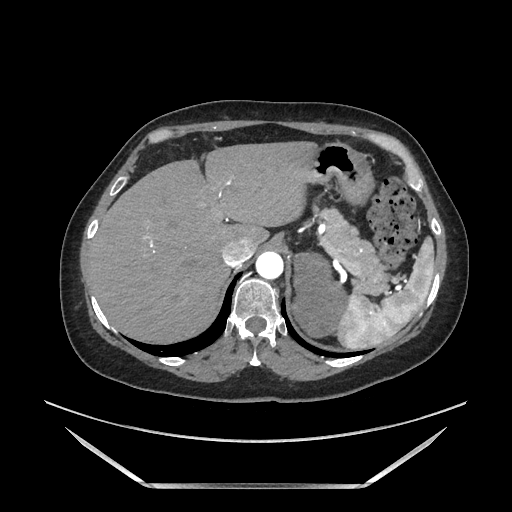
Contrast-enhanced abdominal CT, one axial slice; slice 141 of 205 in the series (ordered by position); soft-tissue window (W 400 / L 40 HU); 1.25 mm slice thickness; 512 × 512 image matrix, field of view 440 × 440 mm. Female patient. From the clinical record (not read from this slice): diagnosis: adrenocortical carcinoma; tumour side: left adrenal; tumour size at pathology: 12.5 cm.
Annotated regions visible in this slice (semi-automatically segmented with operator editing):
- mass: box from (x=294, y=254) to (x=346, y=337) px